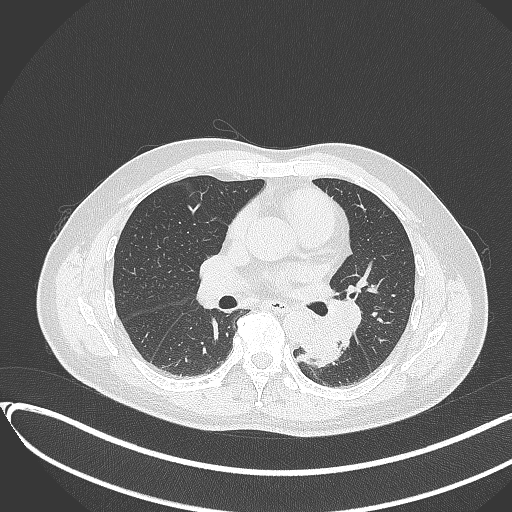
Chest CT, one axial slice; position 184 of 417 along the scan axis; lung window (W 1500 / L -600 HU); 1 mm slice thickness; 512 × 512 image matrix. Patient: male, 54 years. Case-level facts recorded for this patient, not image findings: clinical TNM (as recorded): T3 N0 M0.
Outlined on this slice (bounding box drawn by a radiologist):
- lung tumour (recorded histology: squamous cell carcinoma): bounding box [x1, y1, x2, y2] px = [297, 321, 344, 368]